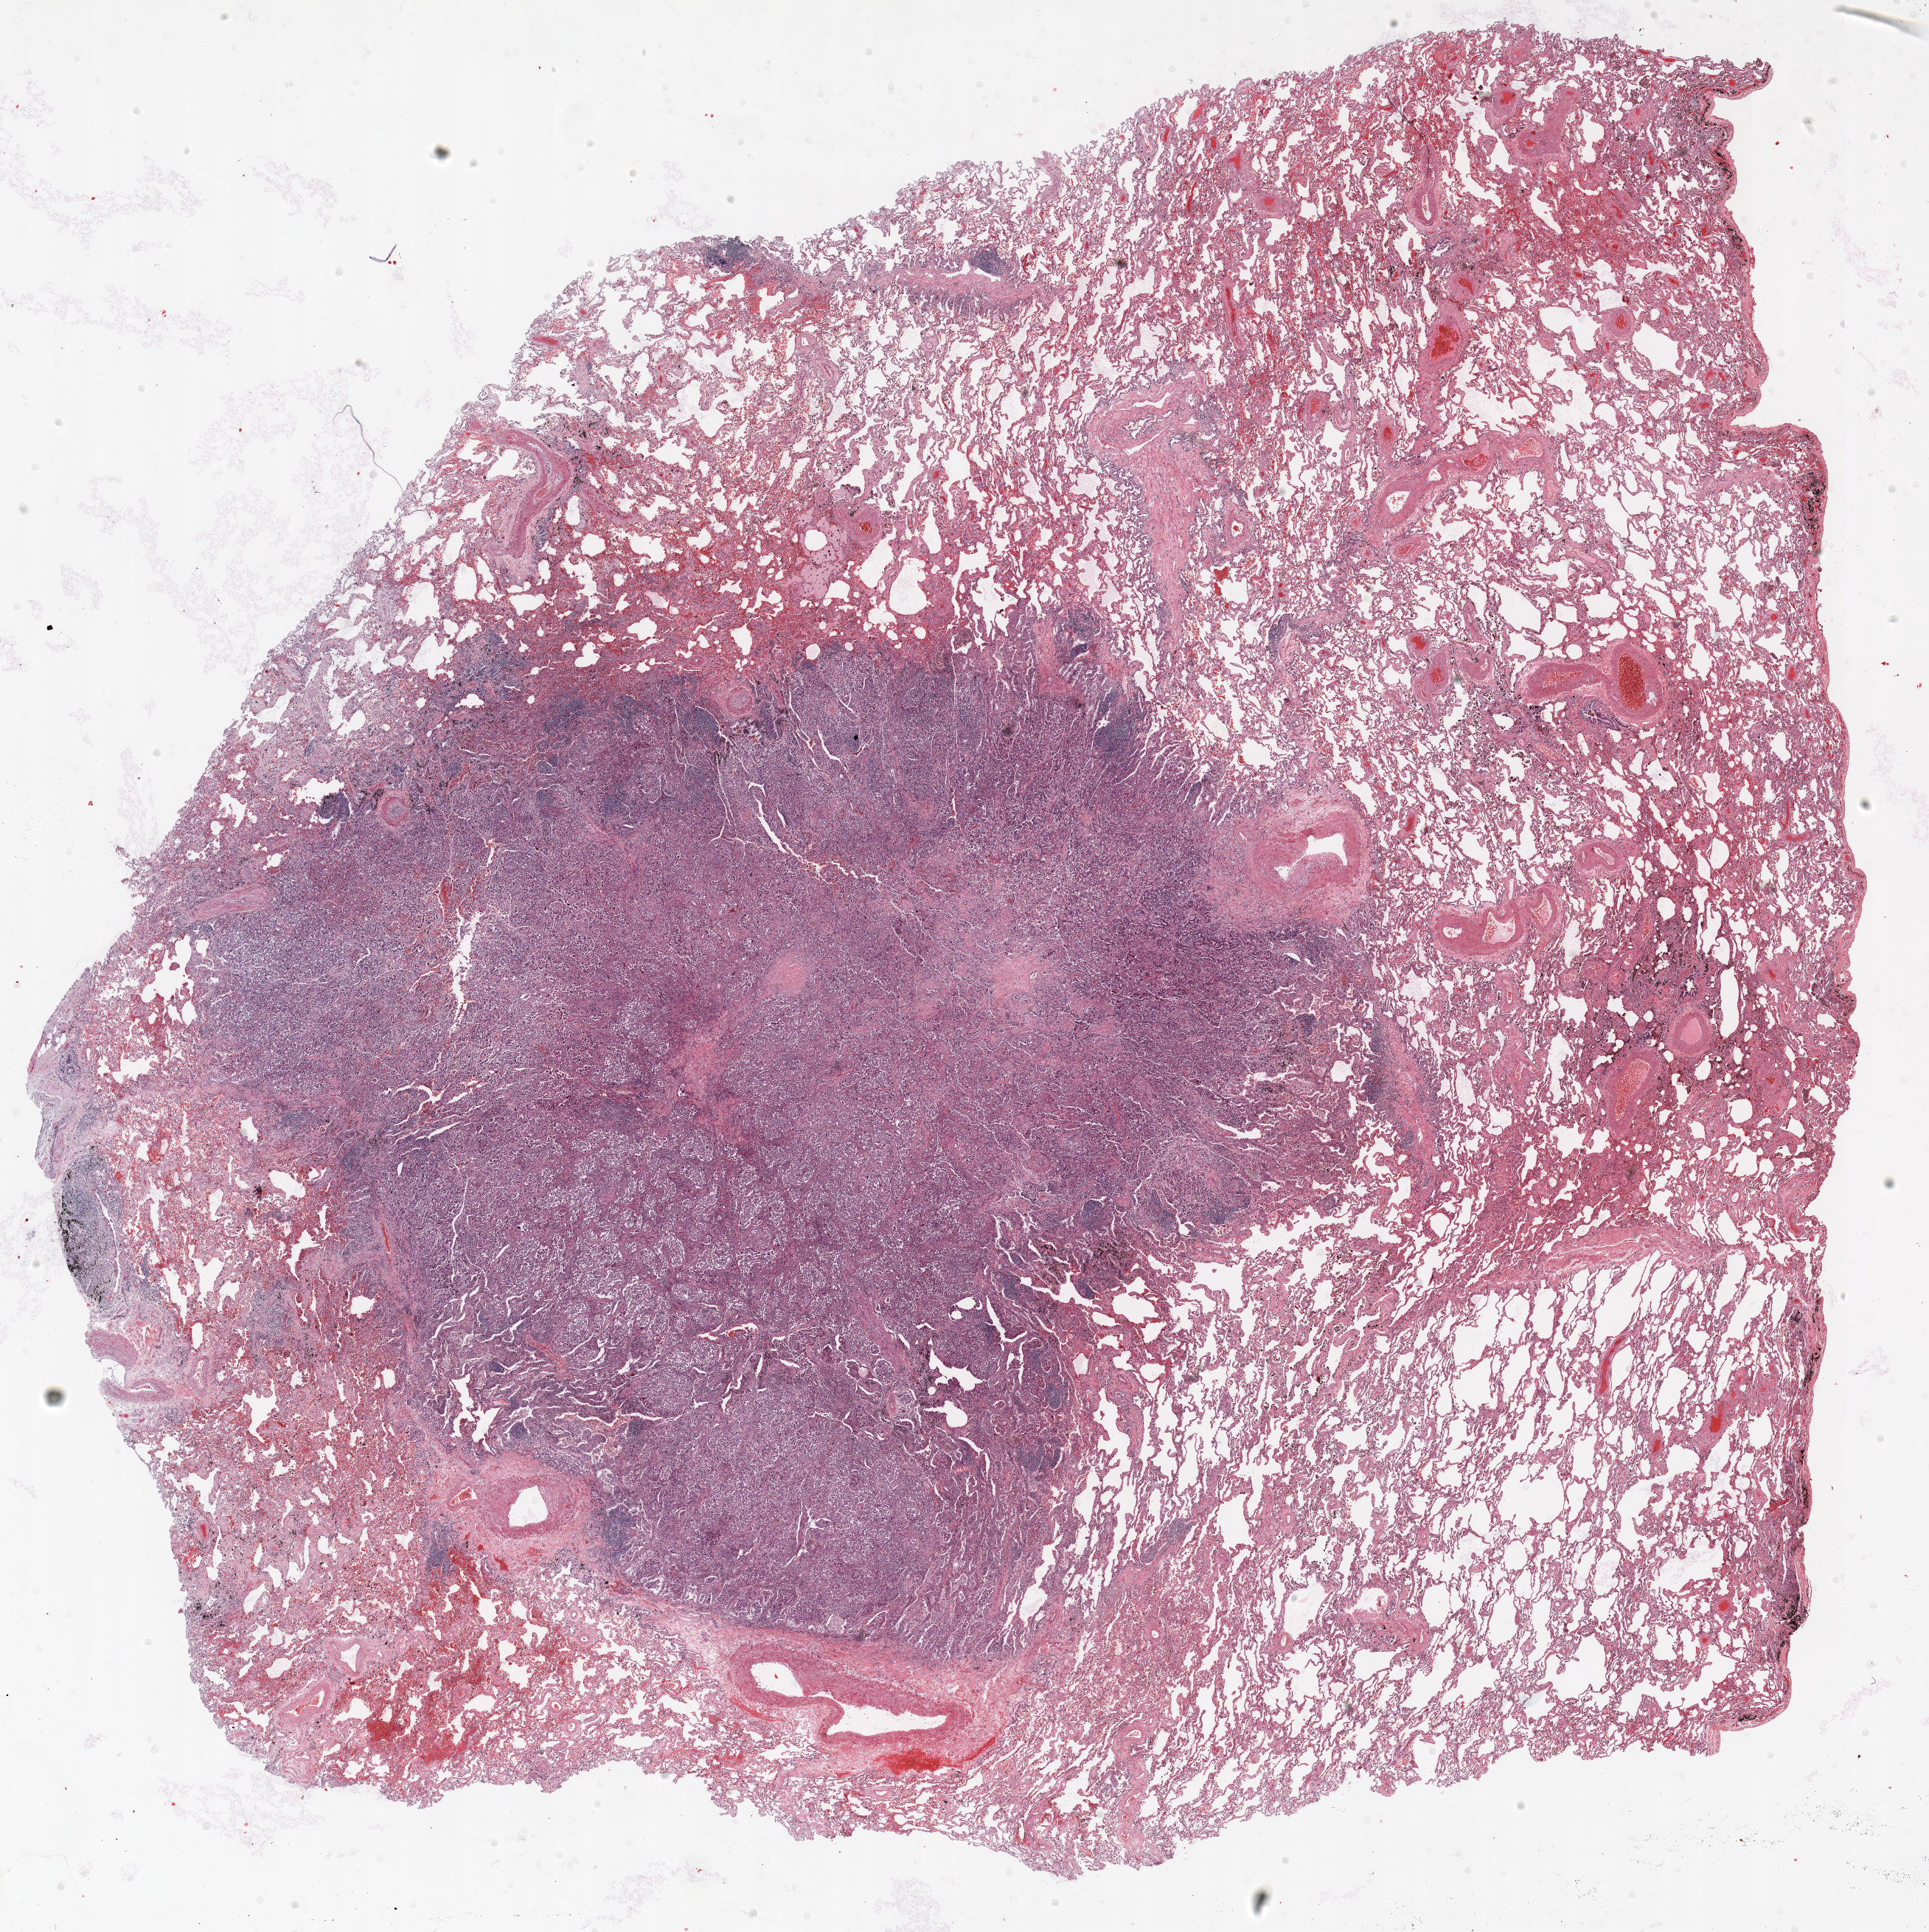
Whole-slide histology image, Hematoxylin and eosin (H&E) stained, whole scanned area (about 21.0 x 21.1 mm, from a 20x scan) shown as a low-resolution overview. Formalin-fixed paraffin-embedded (FFPE) section. Lung. Male patient, aged 64 at enrolment. Current smoker at enrolment. Grade: poorly differentiated (G3).
ICD-O-3 topography: upper lobe of lung (C34.1). Stage (AJCC 6th edition): IA. Primary tumour location (clinical record): left upper lobe. Tumour size (pathology): 15 mm. Participant's lung-cancer diagnosis: Adenocarcinoma, NOS.